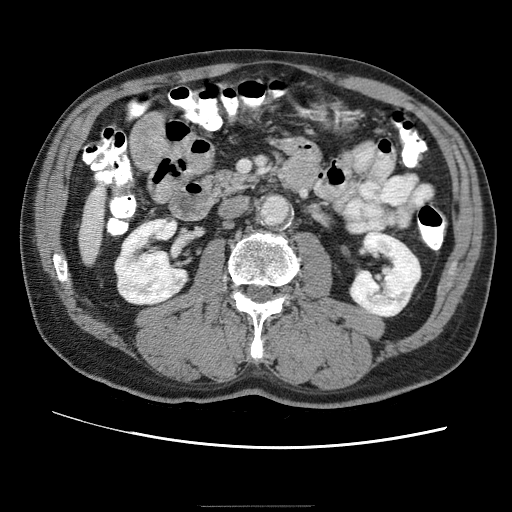
Contrast-enhanced abdominal CT (liver protocol), one axial slice; slice 4 of 75 in the series (ordered by position); reconstruction kernel STANDARD; 120 kVp; one of 2 acquisitions stored at this slice position; soft-tissue window (W 400 / L 40 HU); 512 × 512 image matrix, field of view 360 × 360 mm. Case-level facts recorded for this patient, not image findings: diagnosis: hepatocellular carcinoma (patient treated with transarterial chemoembolisation; whether this scan precedes or follows treatment is not stated here); TNM stage (as recorded): Stage-II; Child-Pugh class: A; tumour differentiation: well differentiated; tumour nodularity: multinodular.
Structures marked on this image (semi-automatic segmentation, software-assisted and operator-edited):
- liver parenchyma outside the tumour (the mass and vessels are separate outlines, so this box may not span the whole liver): box from (x=82, y=200) to (x=94, y=245) px
- liver vessels: (x=85, y=202)–(x=92, y=239)